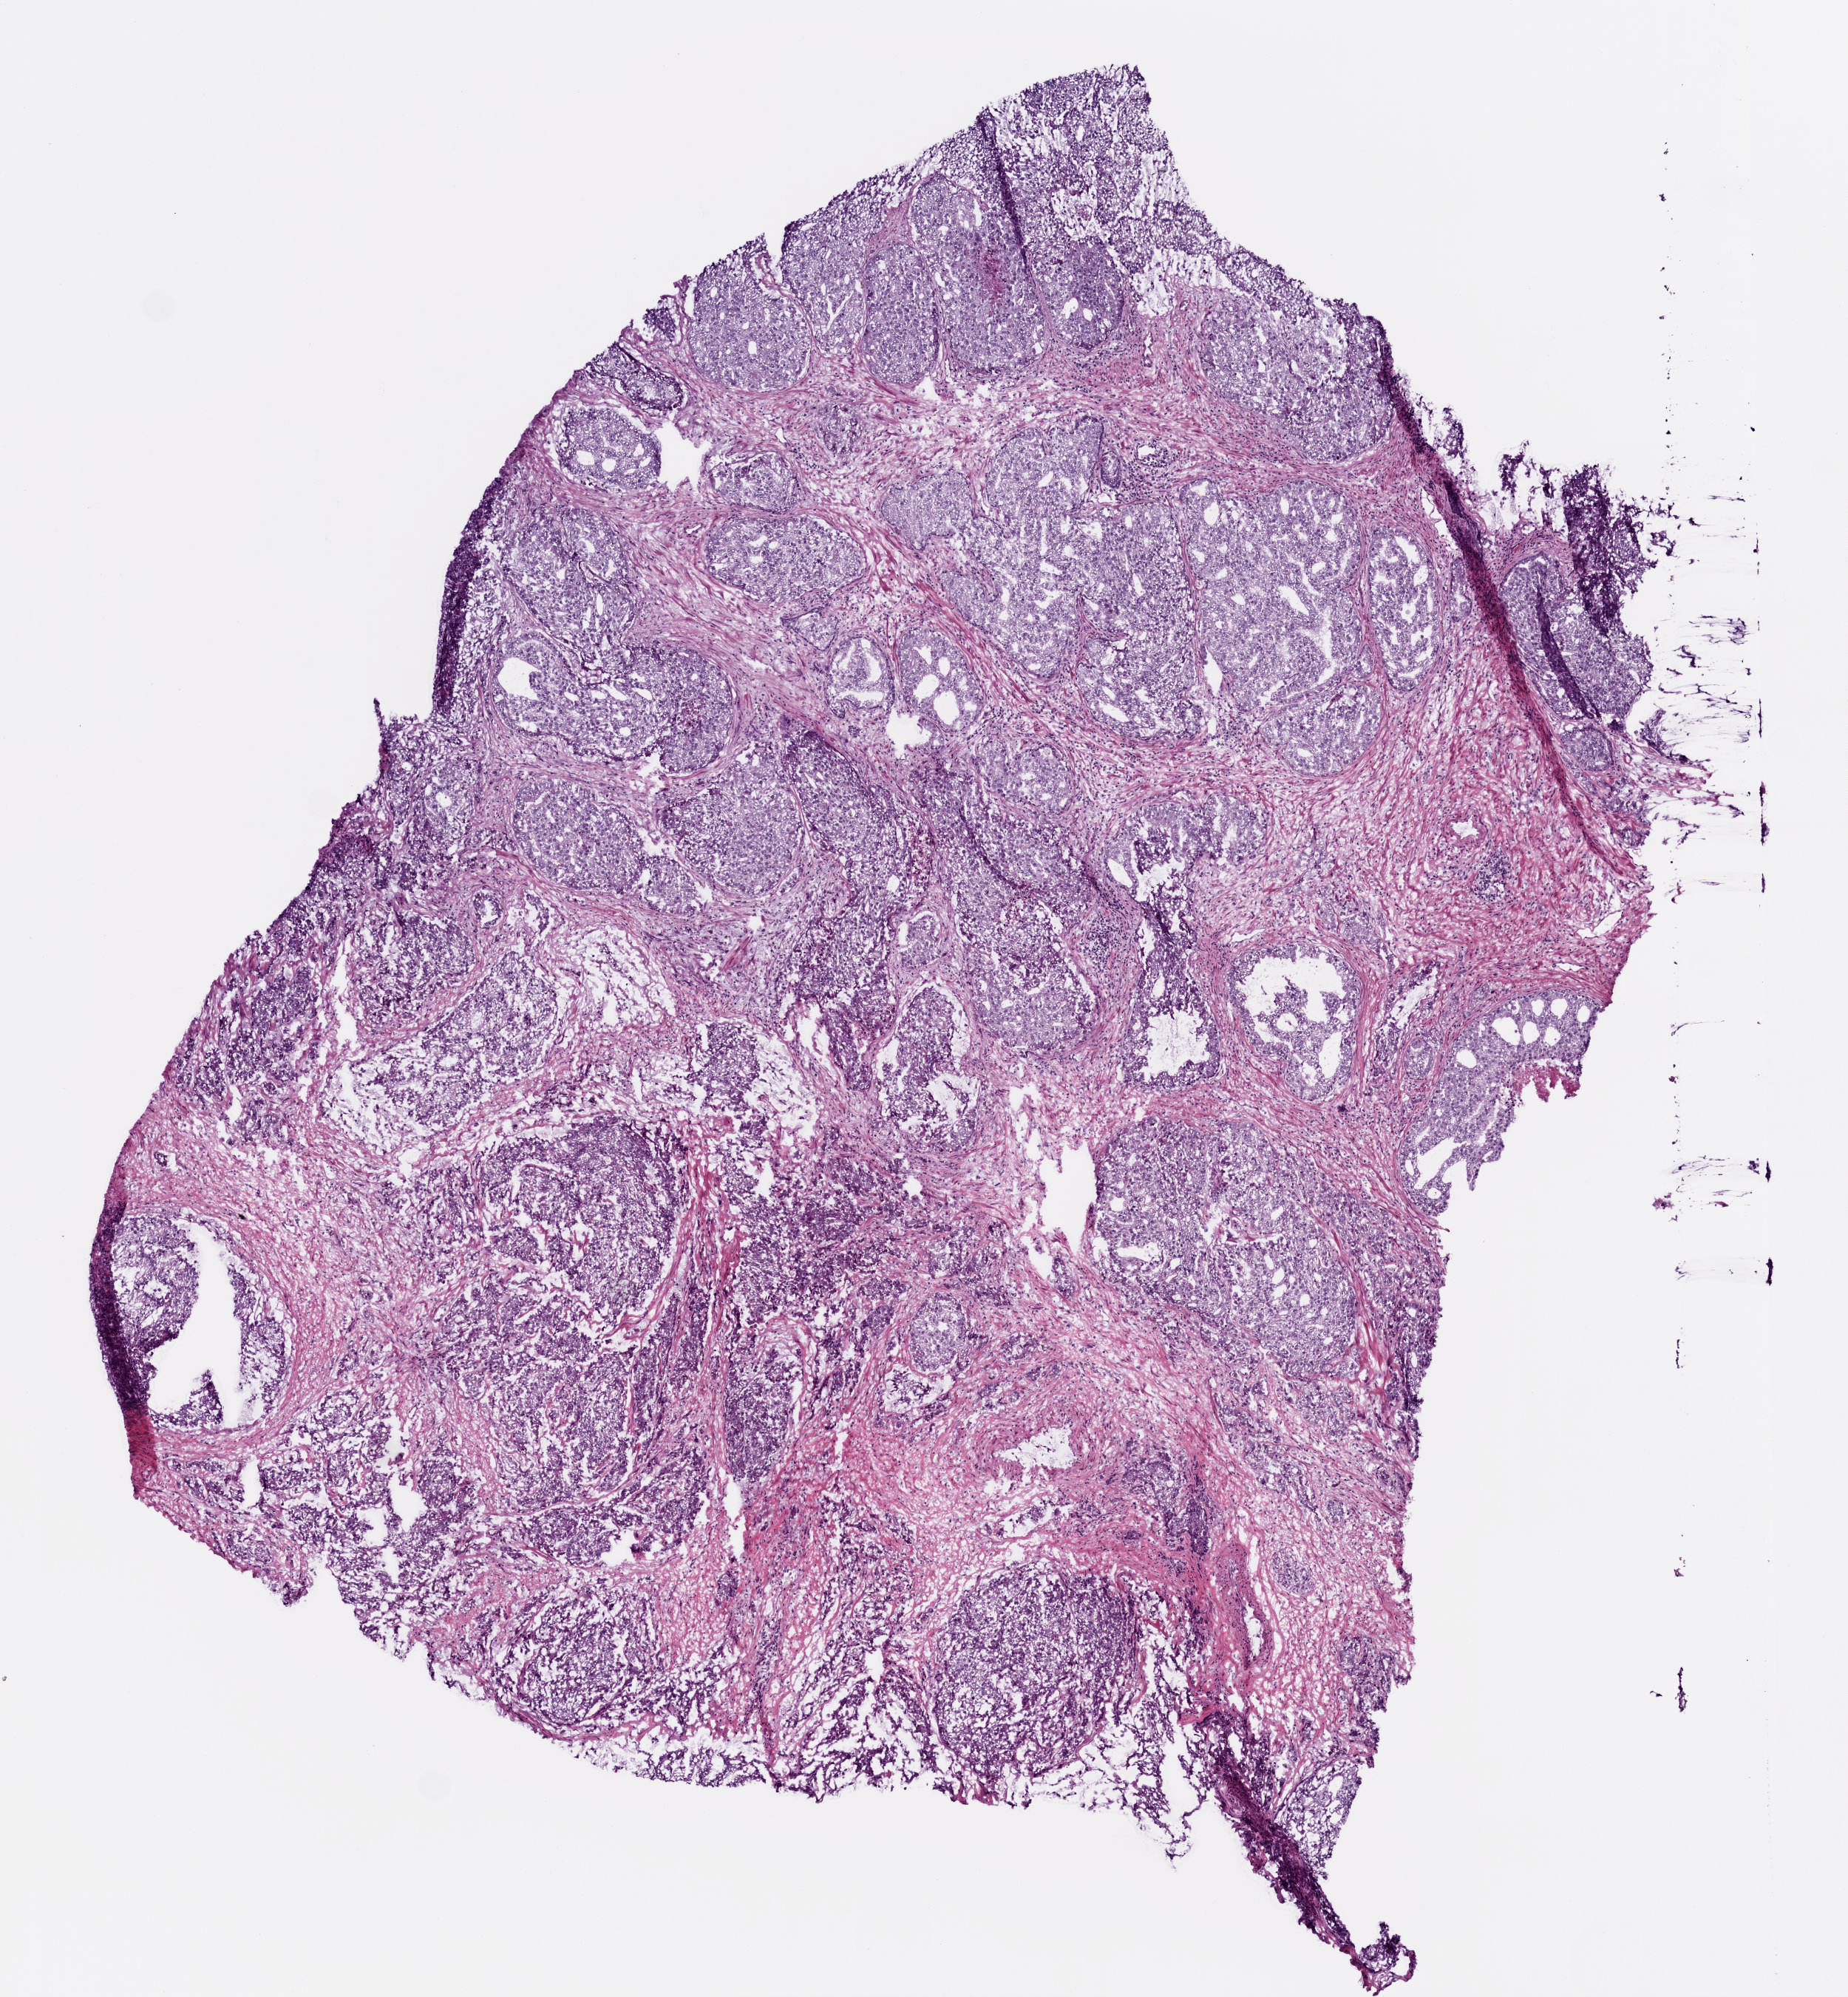
Whole-slide histology image, H&E, shown as a low-resolution overview of the whole scanned area (about 5.0 x 5.4 mm), frozen section from the bottom of the tissue portion, prostate, primary tumour sample. Male patient; age at initial diagnosis 69 years. Gleason score: 7 (4+3). Slide review estimates, as recorded: tumour cells 75%, tumour nuclei 75%, normal cells 2%, stromal cells 18%, necrosis 5%. Infiltration values recorded for this section: lymphocyte infiltration 3%, monocyte infiltration 3%, neutrophil infiltration 0%.
- pathologic diagnosis: Acinar cell carcinoma (prostate gland)
- laterality: bilateral